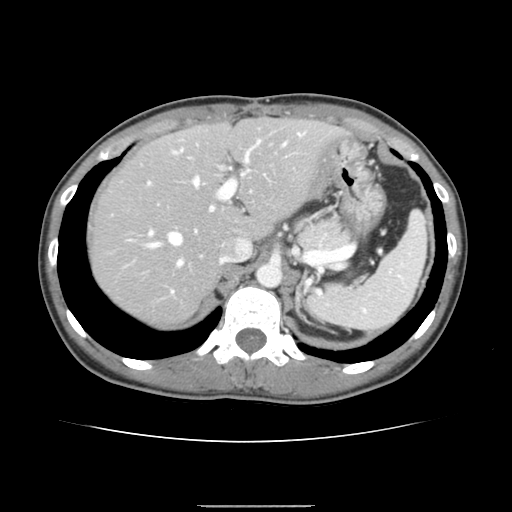
Contrast-enhanced abdominal CT, one axial slice. Position 107 of 150 along the scan axis. Soft-tissue window (W 400 / L 40 HU). 2.5 mm slice thickness. 512 × 512 image matrix, field of view 324 × 324 mm. Female patient, age 32 years. Case-level facts recorded for this patient, not image findings: diagnosis: colorectal cancer liver metastases, imaged before liver resection; multiple liver metastases: yes; largest metastasis: 0.7 cm; disease in both lobes: no.
Annotated regions visible in this slice (manually delineated by an expert):
- hepatic veins: bounding box [x1, y1, x2, y2] px = [150, 178, 199, 265]
- liver: [91, 120, 339, 325]
- planned liver remnant (the part of the liver to remain after resection): [91, 120, 339, 280]
- portal vein (with intrahepatic branches): [148, 132, 305, 292]